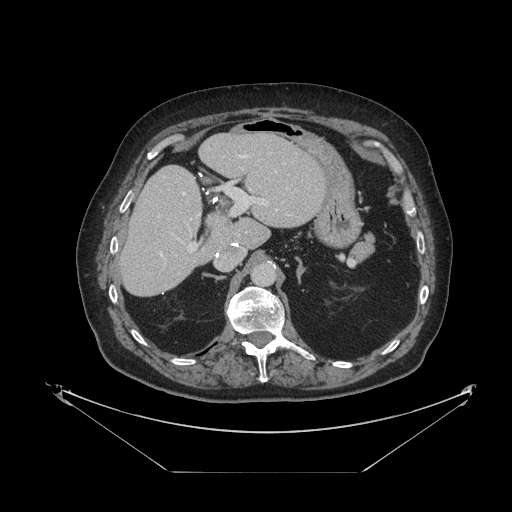
Contrast-enhanced abdominal CT, one axial slice; slice 65 of 121 in the series (ordered by position); 120 kVp; intravenous contrast given; soft-tissue window (W 400 / L 40 HU); 2.5 mm slice thickness; 512 × 512 image matrix, field of view 500 × 500 mm. Male patient, age 68 years. From the clinical record (not read from this slice): diagnosis: colorectal cancer liver metastases, imaged before liver resection; multiple liver metastases: no; largest metastasis: 4 cm; disease in both lobes: no.
Structures marked on this image (expert manual segmentation):
- hepatic veins: box from (x=160, y=155) to (x=288, y=256) px
- liver: (x=121, y=134)–(x=326, y=296)
- planned liver remnant (the part of the liver to remain after resection): (x=121, y=134)–(x=326, y=296)
- portal vein (with intrahepatic branches): (x=182, y=184)–(x=284, y=252)